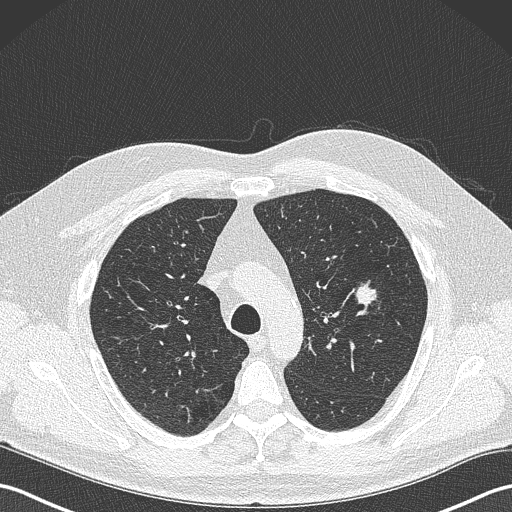
Low-dose screening chest CT, one axial slice; slice 251 of 343 in the series (ordered by position); reconstruction kernel B50f; lung window (W 1500 / L -600 HU); 1 mm slice thickness; 512 × 512 image matrix, field of view 350 × 350 mm.
Annotated regions visible in this slice (outlined manually by an expert reader):
- lesion 1 (tumor, upper lobe of left lung): box from (x=356, y=281) to (x=377, y=309) px